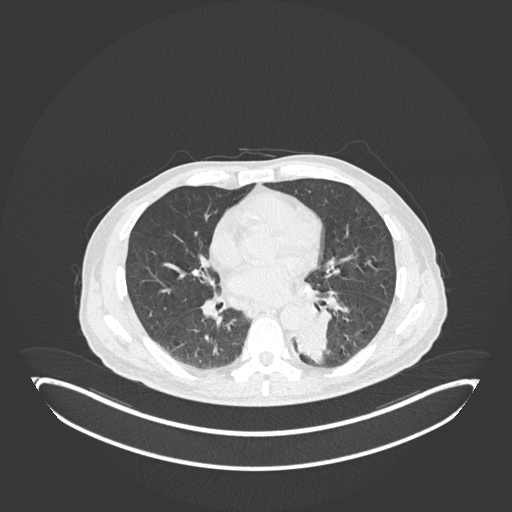
Chest CT, one axial slice; position 88 of 251 along the scan axis; reconstruction kernel B30f; lung window (W 1500 / L -600 HU); 1 mm slice thickness; 512 × 512 image matrix, field of view 500 × 500 mm. Male patient, age 72 years. From the clinical record (not read from this slice): clinical TNM (as recorded): T2b N0 M1.
Annotated regions visible in this slice (bounding box drawn by a radiologist):
- lung tumour (recorded histology: adenocarcinoma): box from (x=291, y=317) to (x=333, y=363) px